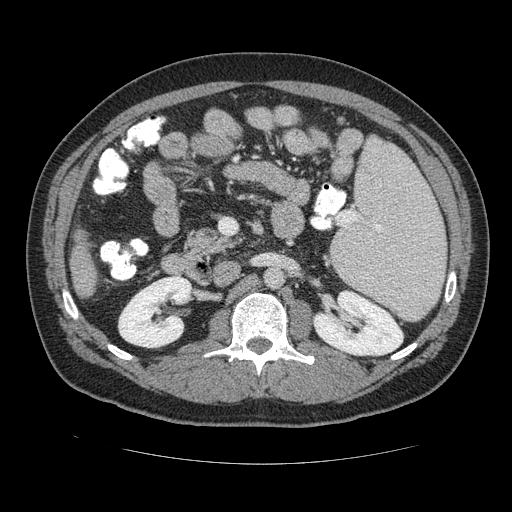
Contrast-enhanced abdominal CT (liver protocol), one axial slice. Position 51 of 113 along the scan axis. Reconstruction kernel STANDARD. 120 kVp. Soft-tissue window (W 400 / L 40 HU). 2.5 mm slice thickness. 512 × 512 image matrix, field of view 400 × 400 mm. Case-level facts recorded for this patient, not image findings: diagnosis: hepatocellular carcinoma (patient treated with transarterial chemoembolisation; whether this scan precedes or follows treatment is not stated here); TNM stage (as recorded): Stage-II; Child-Pugh class: B; tumour size: 4.8 cm.
Structures marked on this image (semi-automatically segmented with operator editing):
- liver parenchyma outside the tumour (the mass and vessels are separate outlines, so this box may not span the whole liver): bounding box <68,224,100,300> (left, top, right, bottom; pixels)